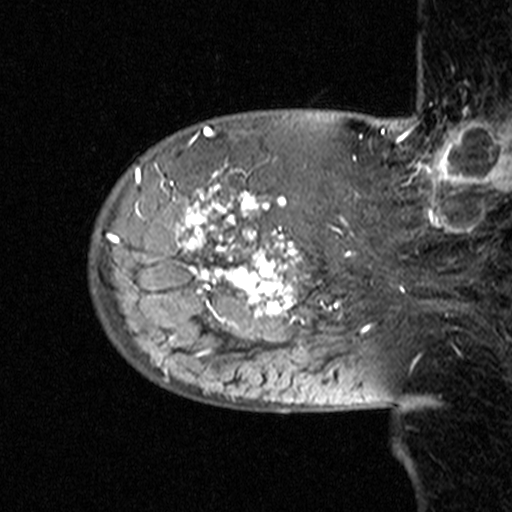
Breast MRI (dynamic contrast-enhanced), one sagittal slice; slice 10 of 44 in the series (ordered by position); dynamic contrast-enhanced study with each time point stored as its own series, time point 2 of 3 at this slice position (early post-contrast, ordered by acquisition time); 1.5 T; TE 4.5 ms, TR 11 ms; 3 mm slice thickness; 512 × 512 image matrix, field of view 200 × 200 mm. Female patient, age 53 years. Case-level facts recorded for this patient, not image findings: setting: breast cancer imaged before/during neoadjuvant chemotherapy; receptor status: HR-positive, HER2-negative.
Structures marked on this image (semi-automatic segmentation, software-assisted and operator-edited):
- analysis volume of interest (the breast-tissue region the enhancement analysis was run in; not a lesion): box from (x=88, y=140) to (x=311, y=353) px
- tumour enhancement mask (voxels above the 90 % enhancement threshold inside the analysis volume of interest): (x=108, y=177)–(x=305, y=324)